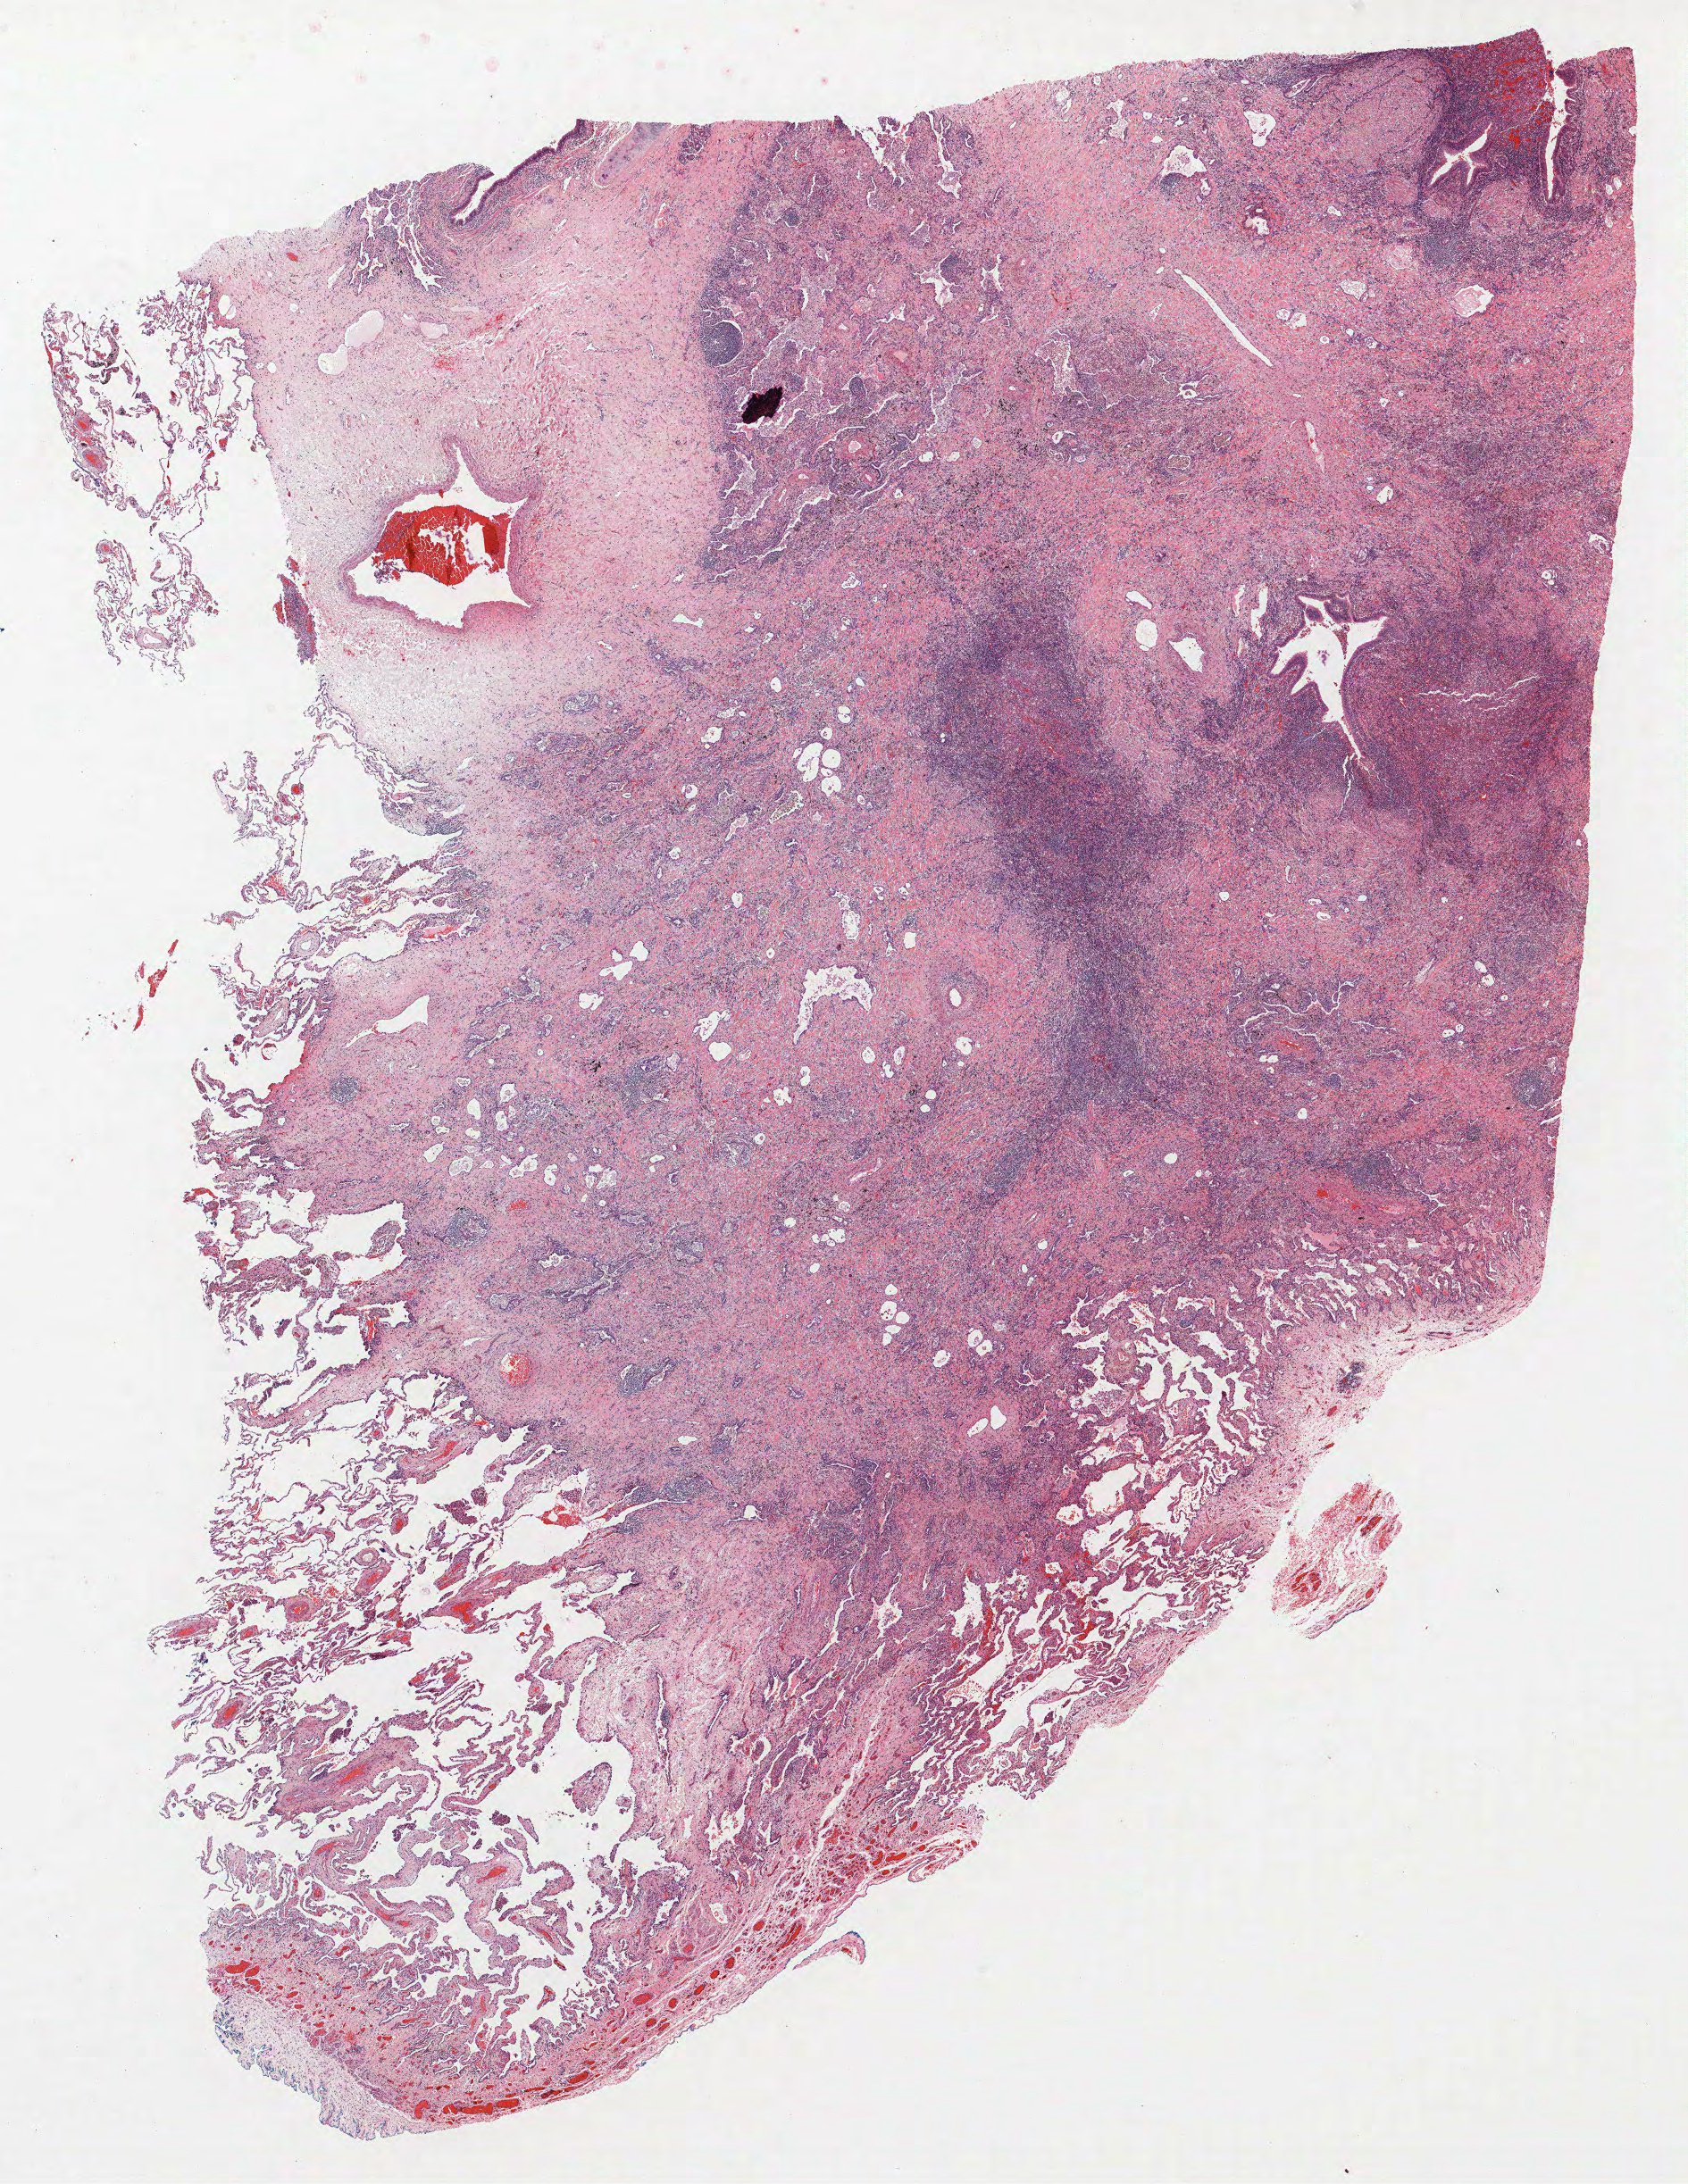
H&E whole-slide image — a low-resolution overview of the entire scanned area, about 15.1 x 19.6 mm (acquisition: 40x scan). Formalin-fixed paraffin-embedded (FFPE) section. Lung. Male, age 58 at enrolment. Current smoker at enrolment. Grade: moderately differentiated (G2).
Tumour size (pathology): 11 mm. Primary tumour location (clinical record): right lower lobe. ICD-O-3 topography: lower lobe of lung (C34.3). Stage (AJCC 6th edition): IA. Participant's lung-cancer diagnosis: Squamous cell carcinoma, large cell, nonkeratinizing, NOS.